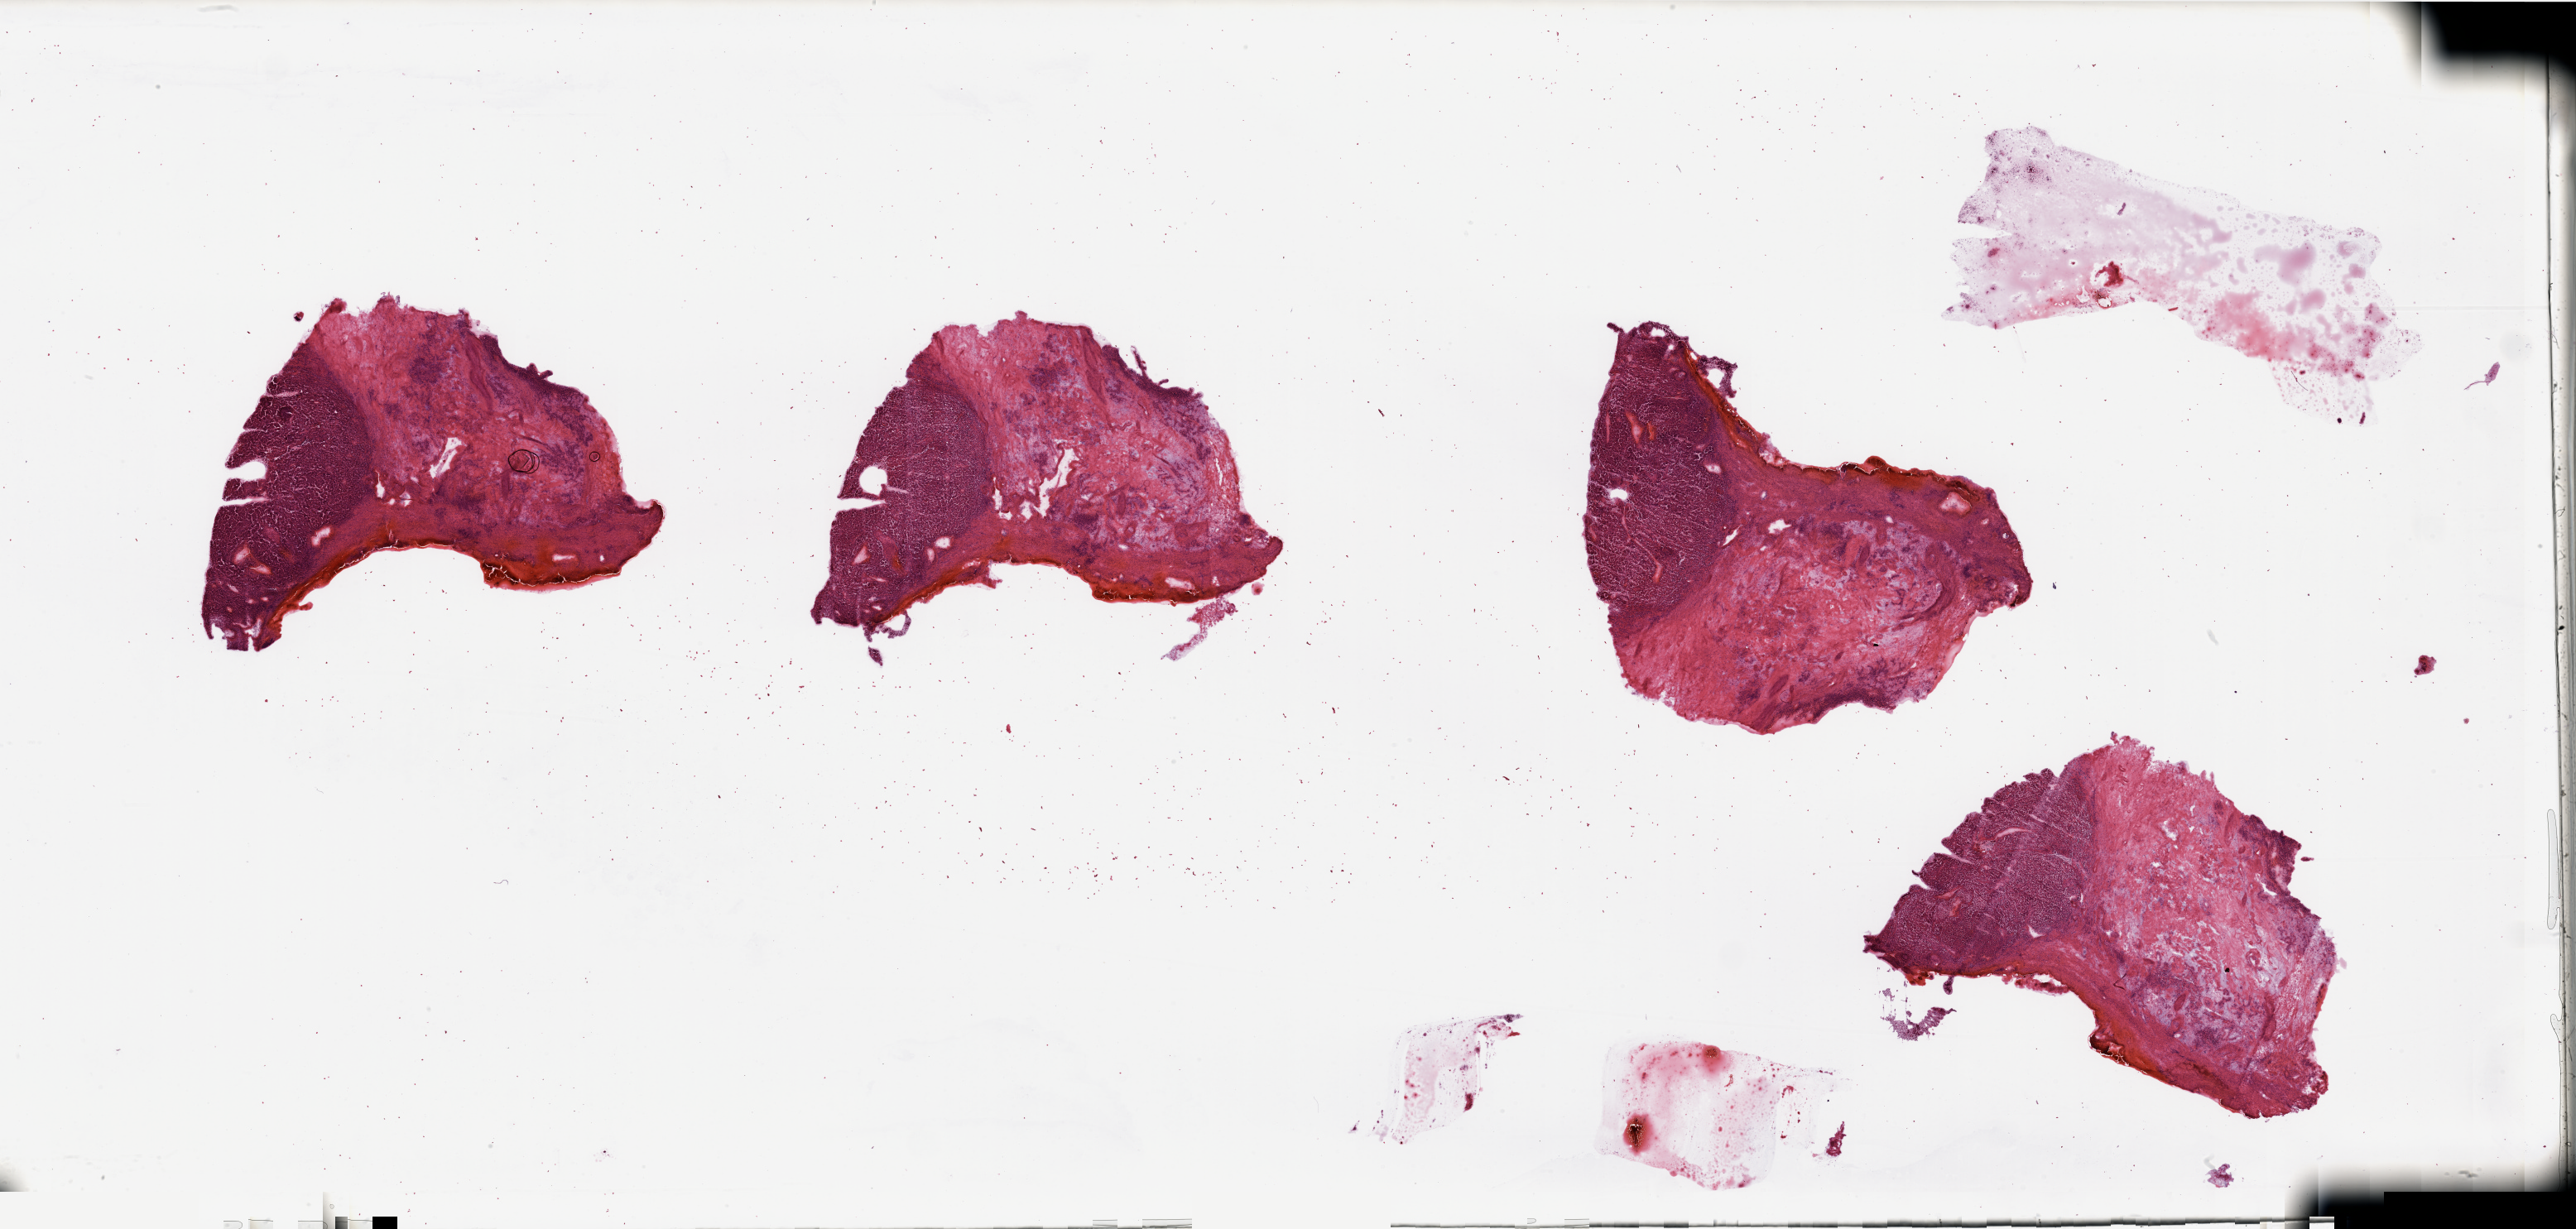
Whole-slide histology image, H&E-stained, a low-resolution overview of the entire scanned area, about 49.2 x 23.5 mm, tumour tissue sample, sampled site: kidney. Male, 78 y/o. Histologic grade: G2 (moderately differentiated). Slide review estimates, as recorded: tumour nuclei 50%, necrosis 20%.
- AJCC pathologic stage: I
- primary tumour site (as recorded): upper pole
- diagnosis: Renal cell carcinoma, NOS